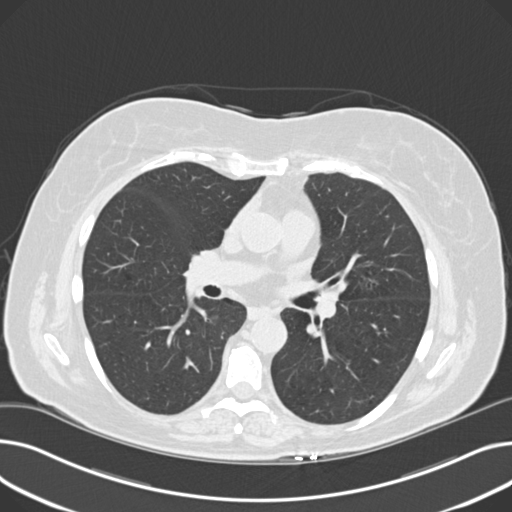
Chest CT (low-dose screening protocol), one axial image. Third screening round (two years after baseline). Lung window (W 1500 / L -600 HU). 120 kVp. Slice 98 of 203 in the series. Female participant, aged 60 years at enrolment.
Expert reader's lesion annotation, bounding box <351,264,391,301> (left, top, right, bottom; pixels). The screening reader recorded 8 non-calcified nodules or masses ≥4 mm on this exam; which of them this box marks is not recorded.